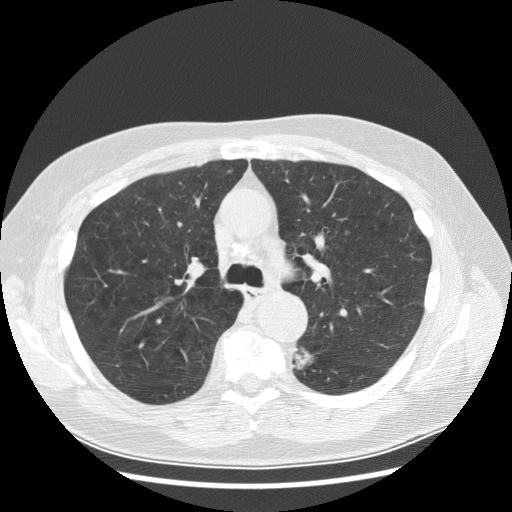
Chest CT (low-dose screening protocol), one axial image. Baseline screening round. Lung window (W 1500 / L -600 HU). 2.5 mm slice thickness. 120 kVp. Slice 91 of 282 in the series. Male, age 70 years at enrolment. Current smoker at enrolment.
Expert-annotated lung lesion, bounding box [x1, y1, x2, y2] px = [276, 339, 324, 379]. The exam's reader record, not a measurement of the box and not confirmed to be the same lesion: non-calcified nodule or mass ≥4 mm, left lower lobe, 27 × 16 mm, spiculated (stellate) margins, soft tissue attenuation, pre-existing on the prior screen: yes; interval growth: yes. Official screen result: positive, change unspecified: nodule(s) >= 4 mm or enlarging nodule(s), mass(es), or other non-specific abnormalities suspicious for lung cancer. Later outcome: lung cancer diagnosed 97 days after this screen — papillary adenocarcinoma, NOS, left lower lobe, moderately differentiated (G2), stage IB (AJCC 6th edition), 35 mm at pathology.